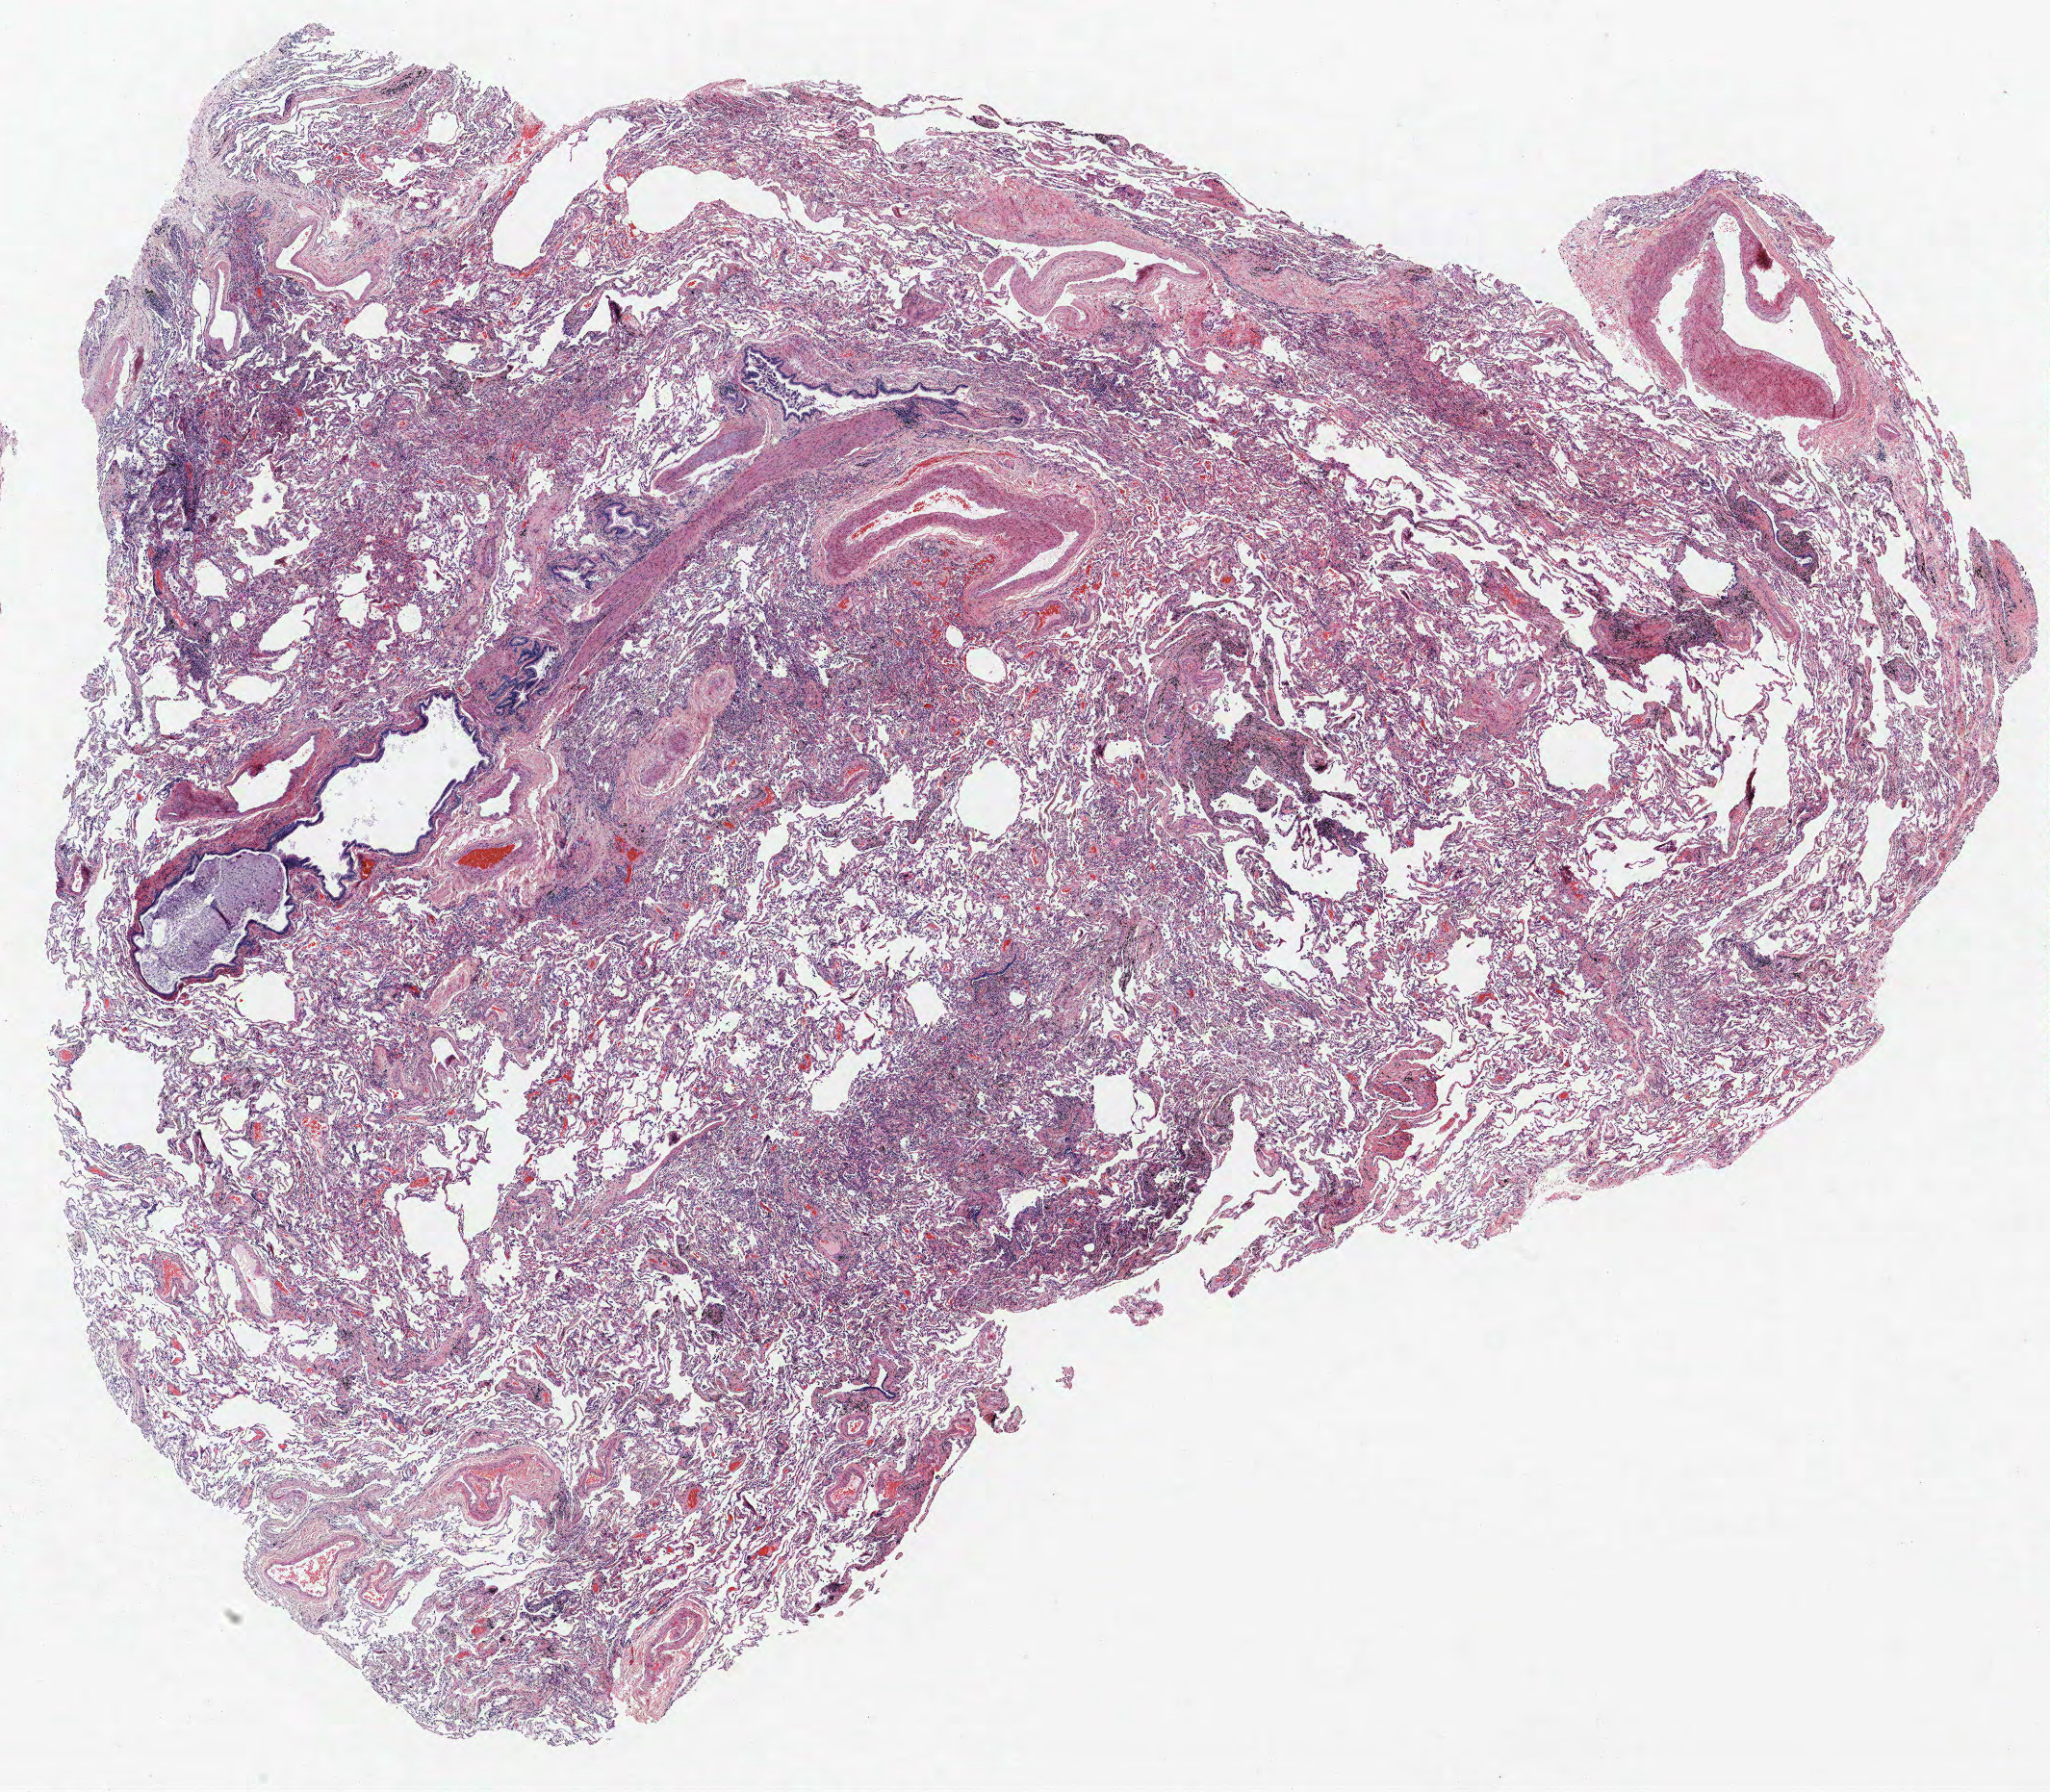
Hematoxylin and eosin (H&E) stained whole-slide image — a low-resolution overview of the entire scanned area, about 17.0 x 14.9 mm, FFPE section, lung tissue. Male patient, aged 63 at enrolment. Former smoker at enrolment. Grade: moderately differentiated (G2).
Primary tumour location (clinical record): left upper lobe. Stage (AJCC 6th edition): IB. Tumour size (pathology): 14 mm. Participant's lung-cancer diagnosis: Adenocarcinoma, NOS.